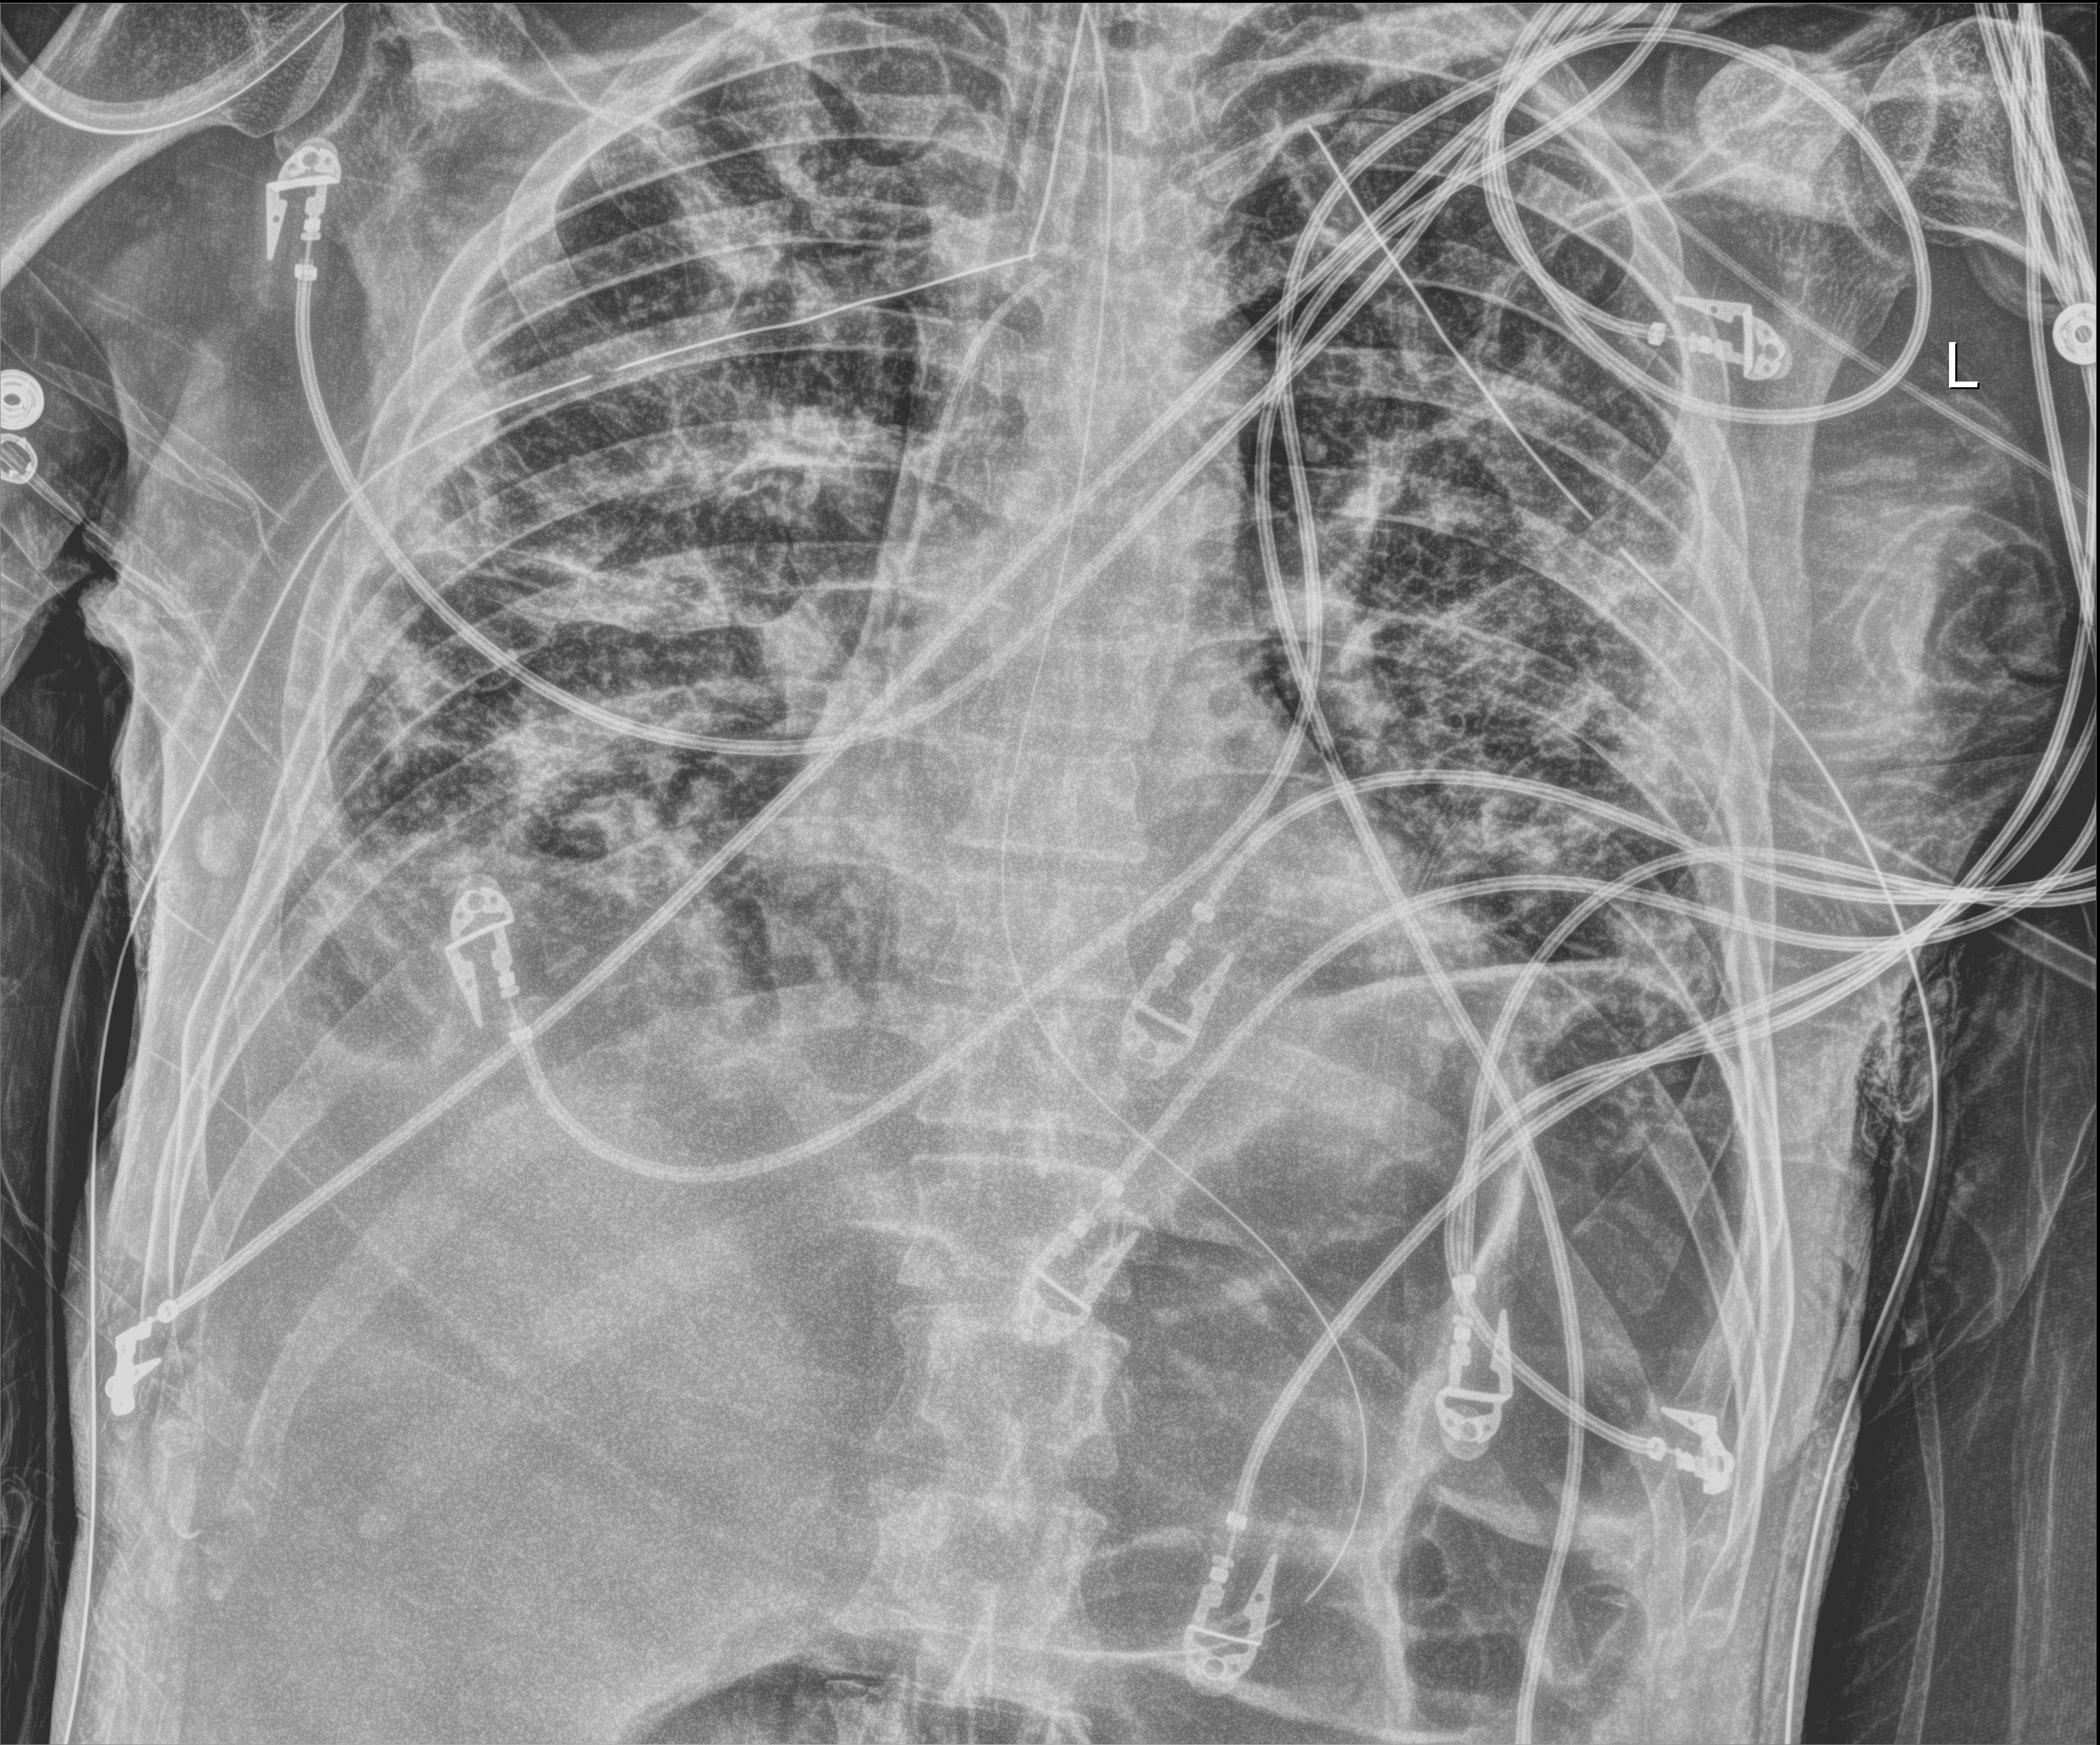
Portable chest radiograph; anteroposterior (AP) projection. Patient hospitalised with COVID-19; male, aged 18–59 years.
Admission-level facts for this patient (not findings on this image; timing relative to this image not recorded): mechanically ventilated during this hospital stay: yes; diabetes (admission record): yes.